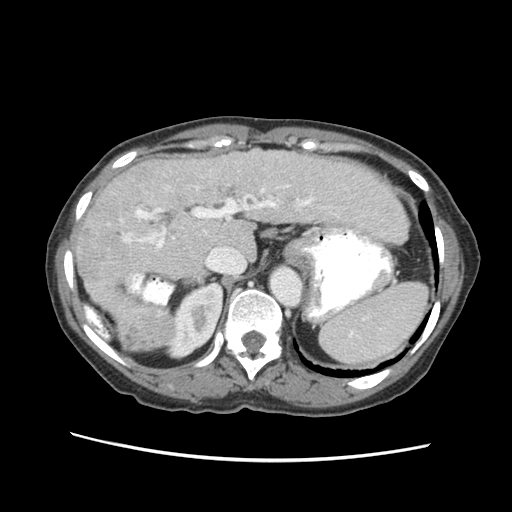
Contrast-enhanced abdominal CT (liver protocol), one axial slice. Slice 41 of 63 in the series (ordered by position). Reconstruction kernel STANDARD. 120 kVp. Soft-tissue window (W 400 / L 40 HU). 2.5 mm slice thickness. 512 × 512 image matrix, field of view 340 × 340 mm. From the clinical record (not read from this slice): diagnosis: hepatocellular carcinoma (patient treated with transarterial chemoembolisation; whether this scan precedes or follows treatment is not stated here); TNM stage (as recorded): Stage-I; Child-Pugh class: B; tumour differentiation: well differentiated; tumour nodularity: uninodular.
Annotated regions visible in this slice (semi-automatic segmentation, software-assisted and operator-edited):
- liver parenchyma outside the tumour (the mass and vessels are separate outlines, so this box may not span the whole liver): box from (x=74, y=146) to (x=410, y=350) px
- mass: (x=116, y=308)–(x=177, y=353)
- liver vessels: (x=123, y=184)–(x=330, y=250)